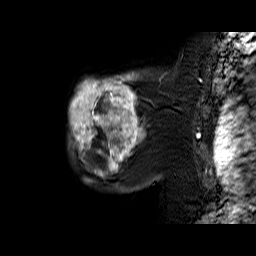
Breast MRI (dynamic contrast-enhanced), one sagittal slice; position 49 of 60 along the scan axis; dynamic contrast-enhanced series, time point 2 of 6 at this slice position (early post-contrast); 1.5 T; TE 6.4 ms, TR 32.9 ms; 4 mm slice thickness; 256 × 256 image matrix, field of view 200 × 200 mm. Female patient. From the clinical record (not read from this slice): setting: breast cancer imaged before/during neoadjuvant chemotherapy; receptor status: triple-negative.
Outlined on this slice (semi-automatic segmentation, software-assisted and operator-edited):
- analysis volume of interest (the breast-tissue region the enhancement analysis was run in; not a lesion): bounding box <69,70,159,174> (left, top, right, bottom; pixels)
- tumour enhancement mask (voxels above the 100 % enhancement threshold inside the analysis volume of interest): <69,72,144,174>